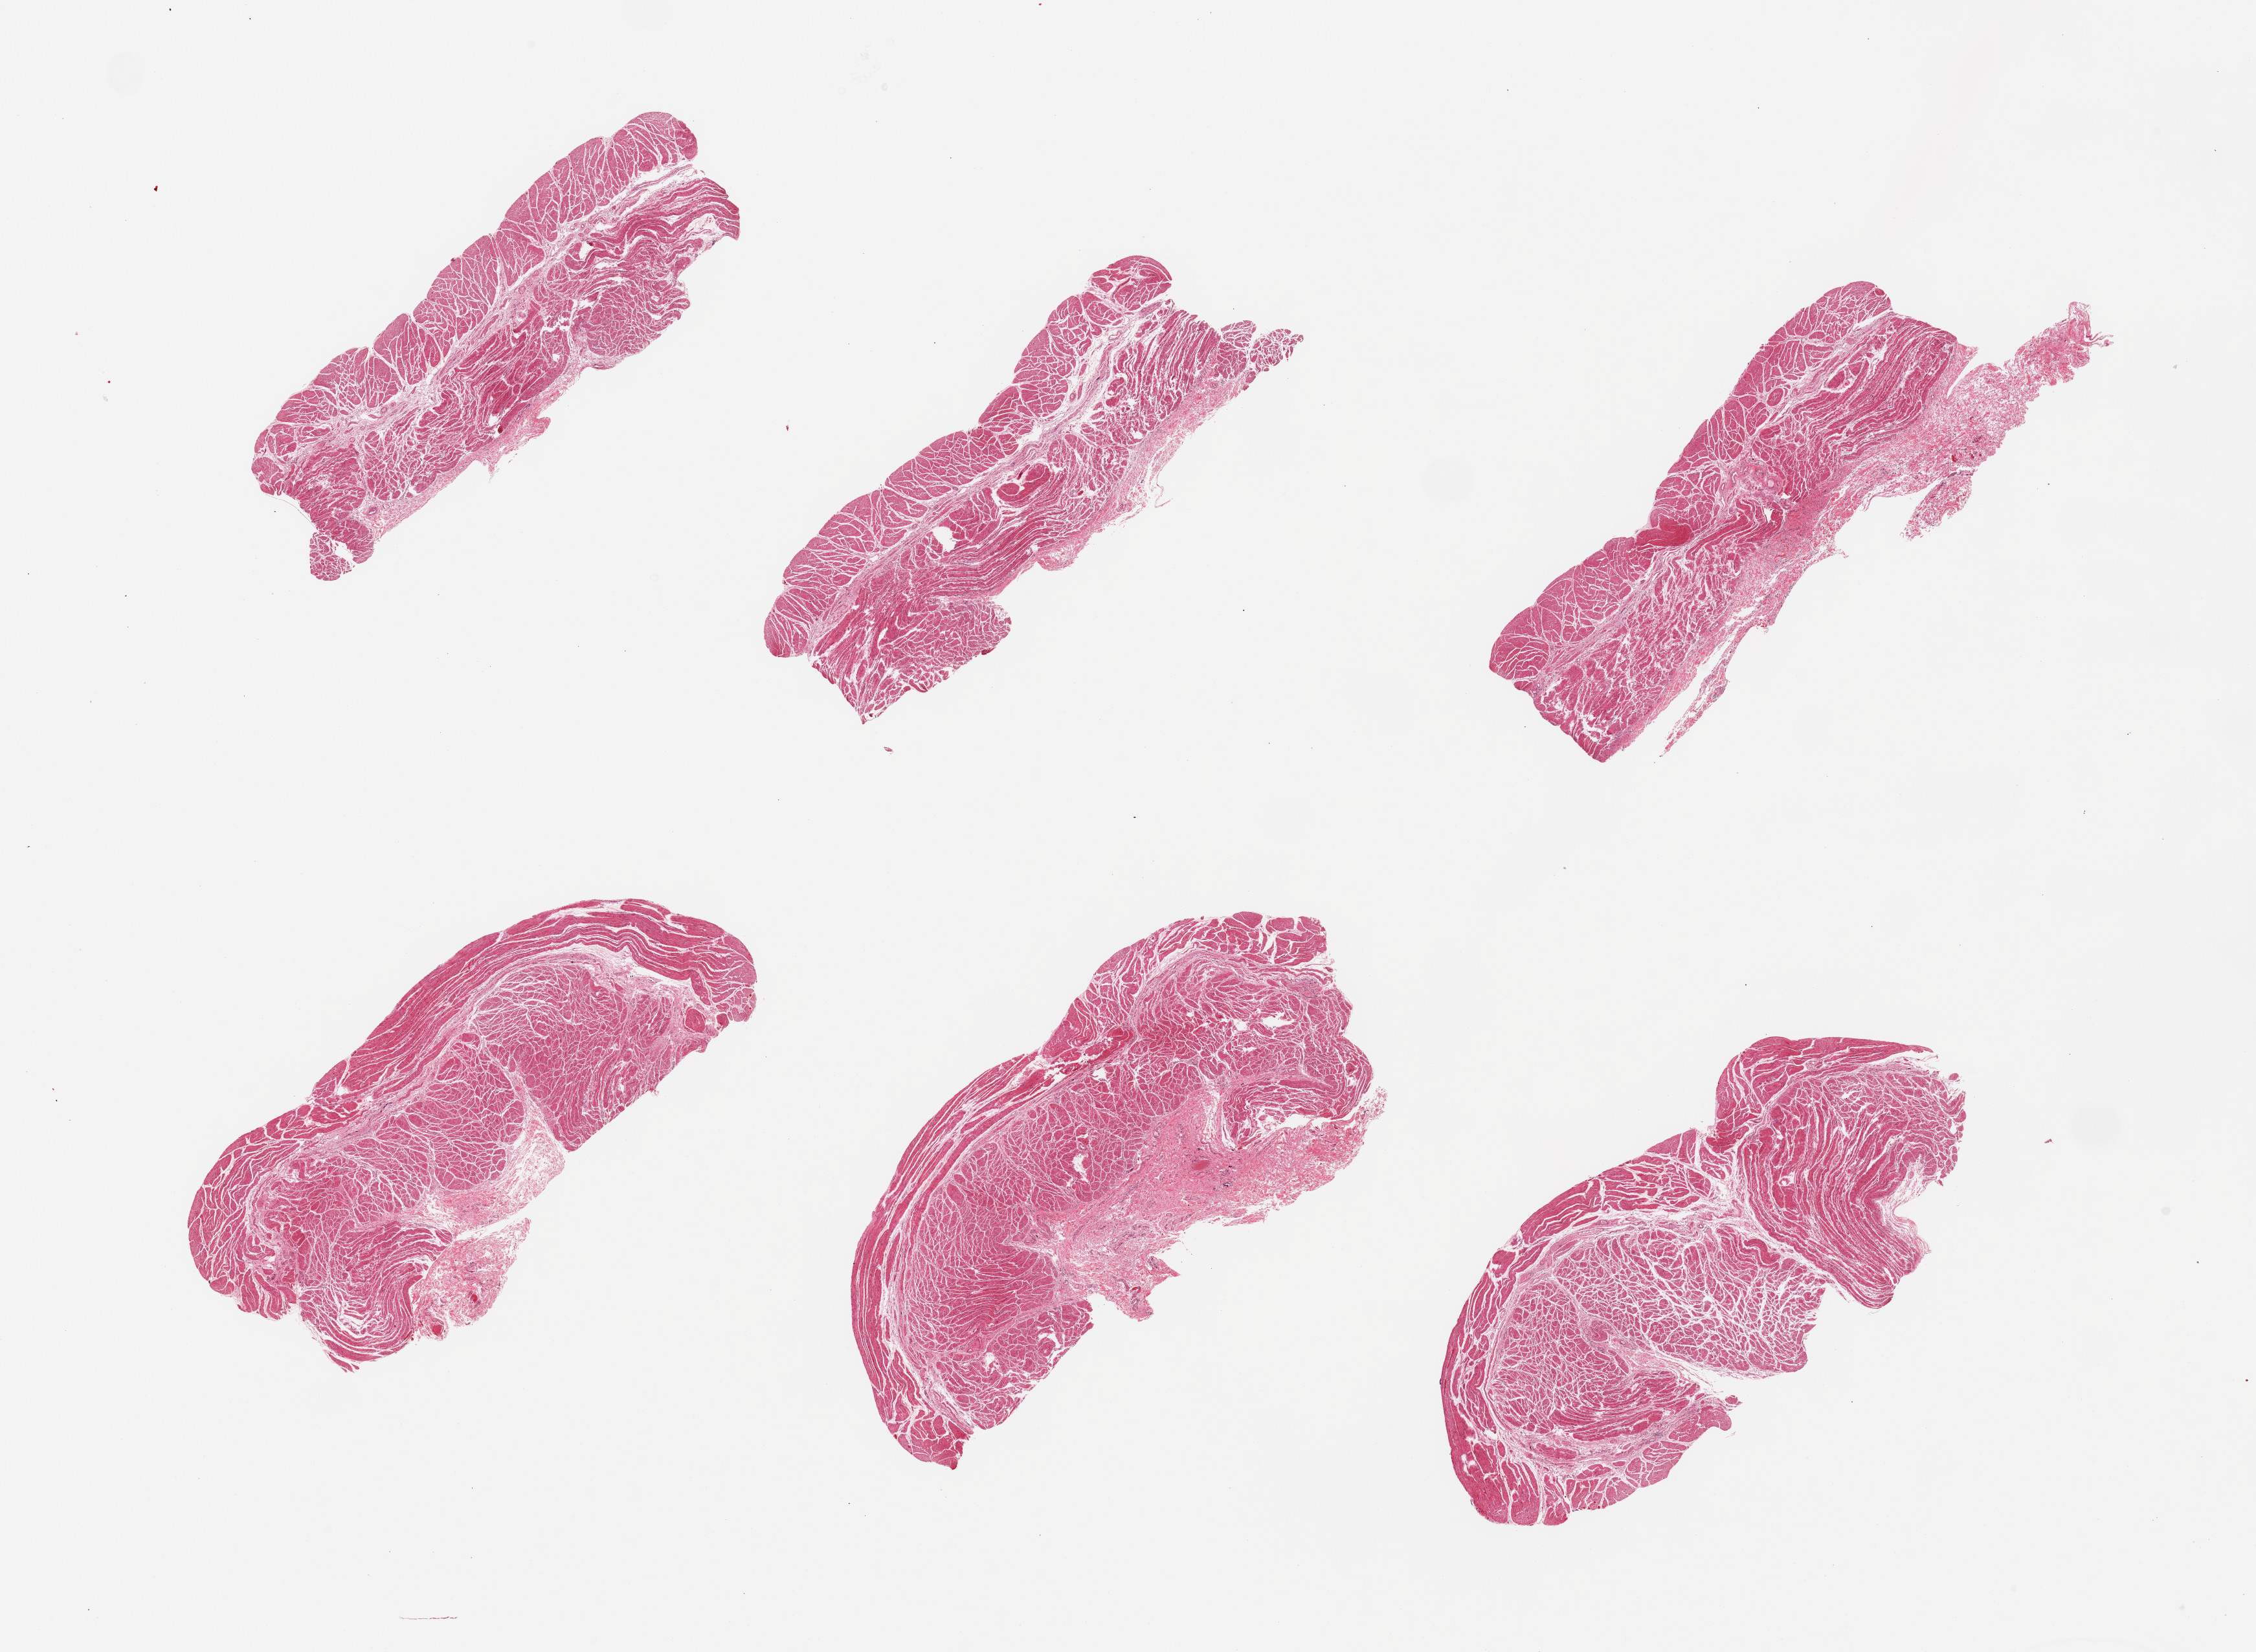
Digitized hematoxylin and eosin (H&E)-stained section, brightfield — a low-resolution overview of the entire scanned area, about 27.6 x 20.2 mm, PAXgene-fixed, paraffin-embedded tissue, sampled site (target tissue): esophageal muscle, tissue donor sample.
Pathologist's review note for this sample: 6 pieces.